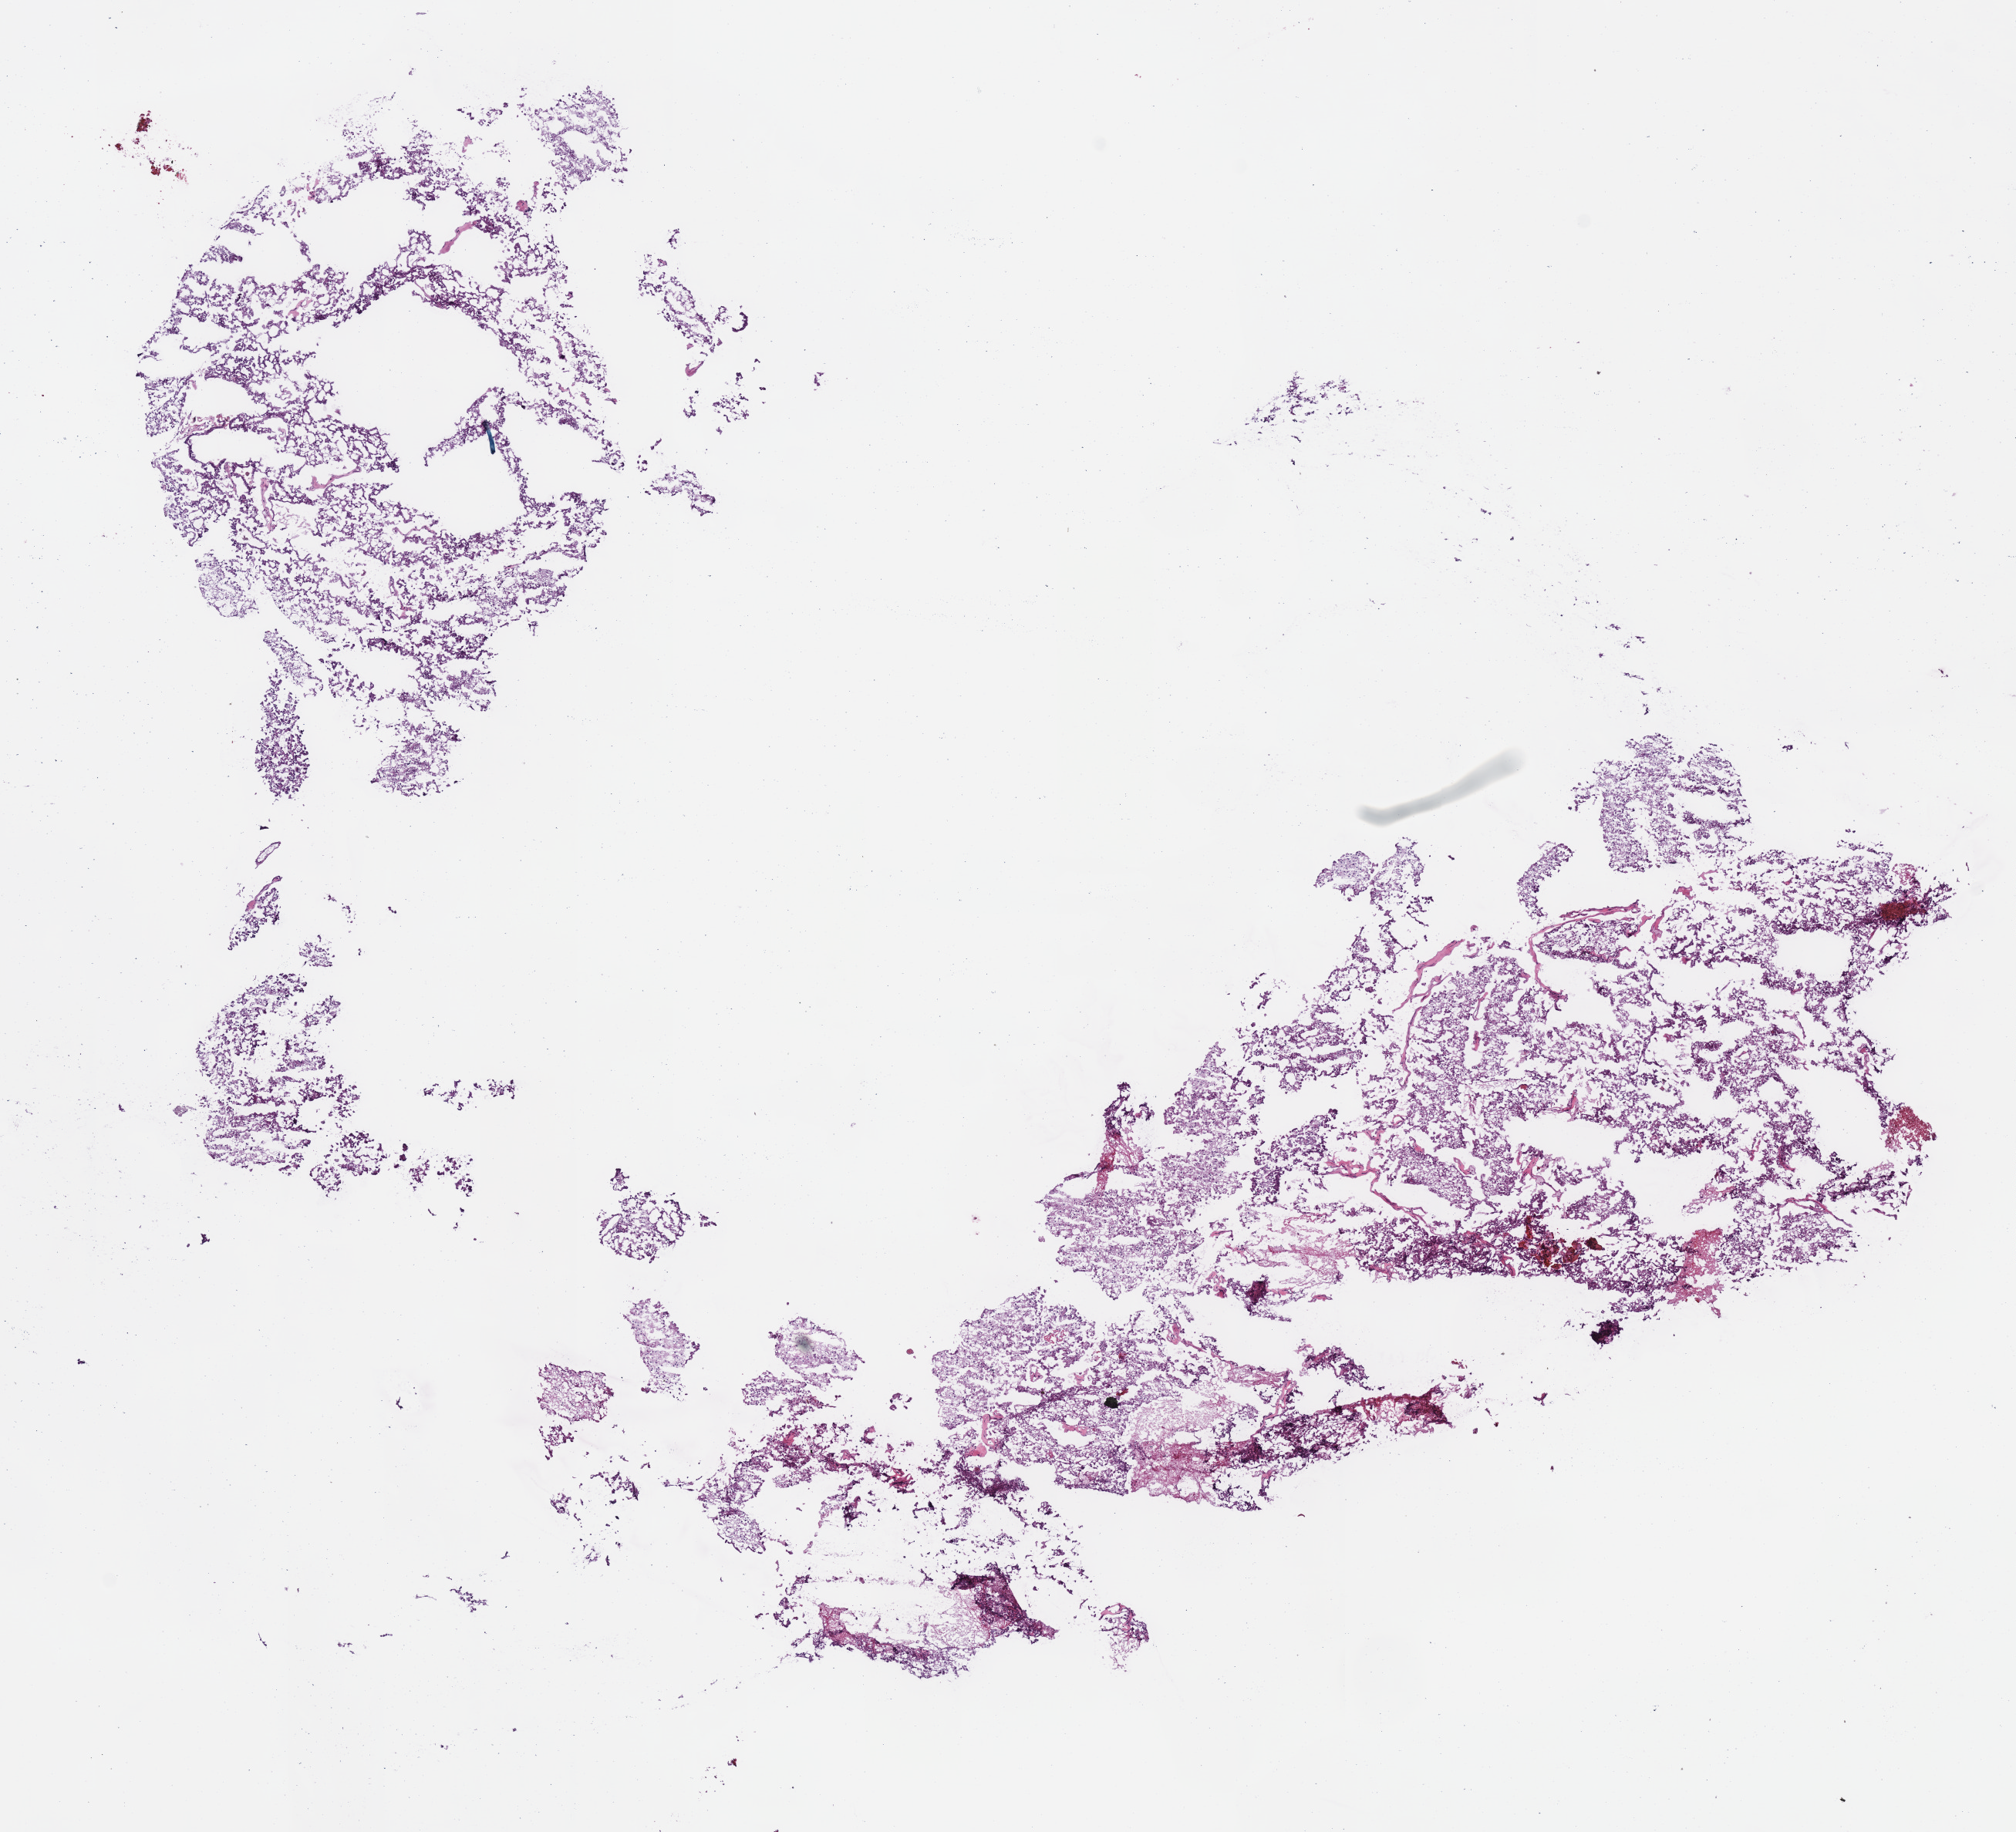
Digitized H&E tissue section (whole slide), low-resolution overview of the scanned area, about 10.3 x 9.3 mm (slide scanned at 40x). Frozen section. Sample: primary tumour, kidney. Female, age 57 years at initial diagnosis. Composition of this section per pathologist review: tumour cells 96%, tumour nuclei 90%, normal cells 0%, stromal cells 0%, necrosis 4%. Inflammatory infiltration, as recorded: lymphocyte infiltration 2%, monocyte infiltration 0%, neutrophil infiltration 0%.
- diagnosis: Renal cell carcinoma, chromophobe type
- AJCC pathologic stage: III (5th edition)
- laterality: right